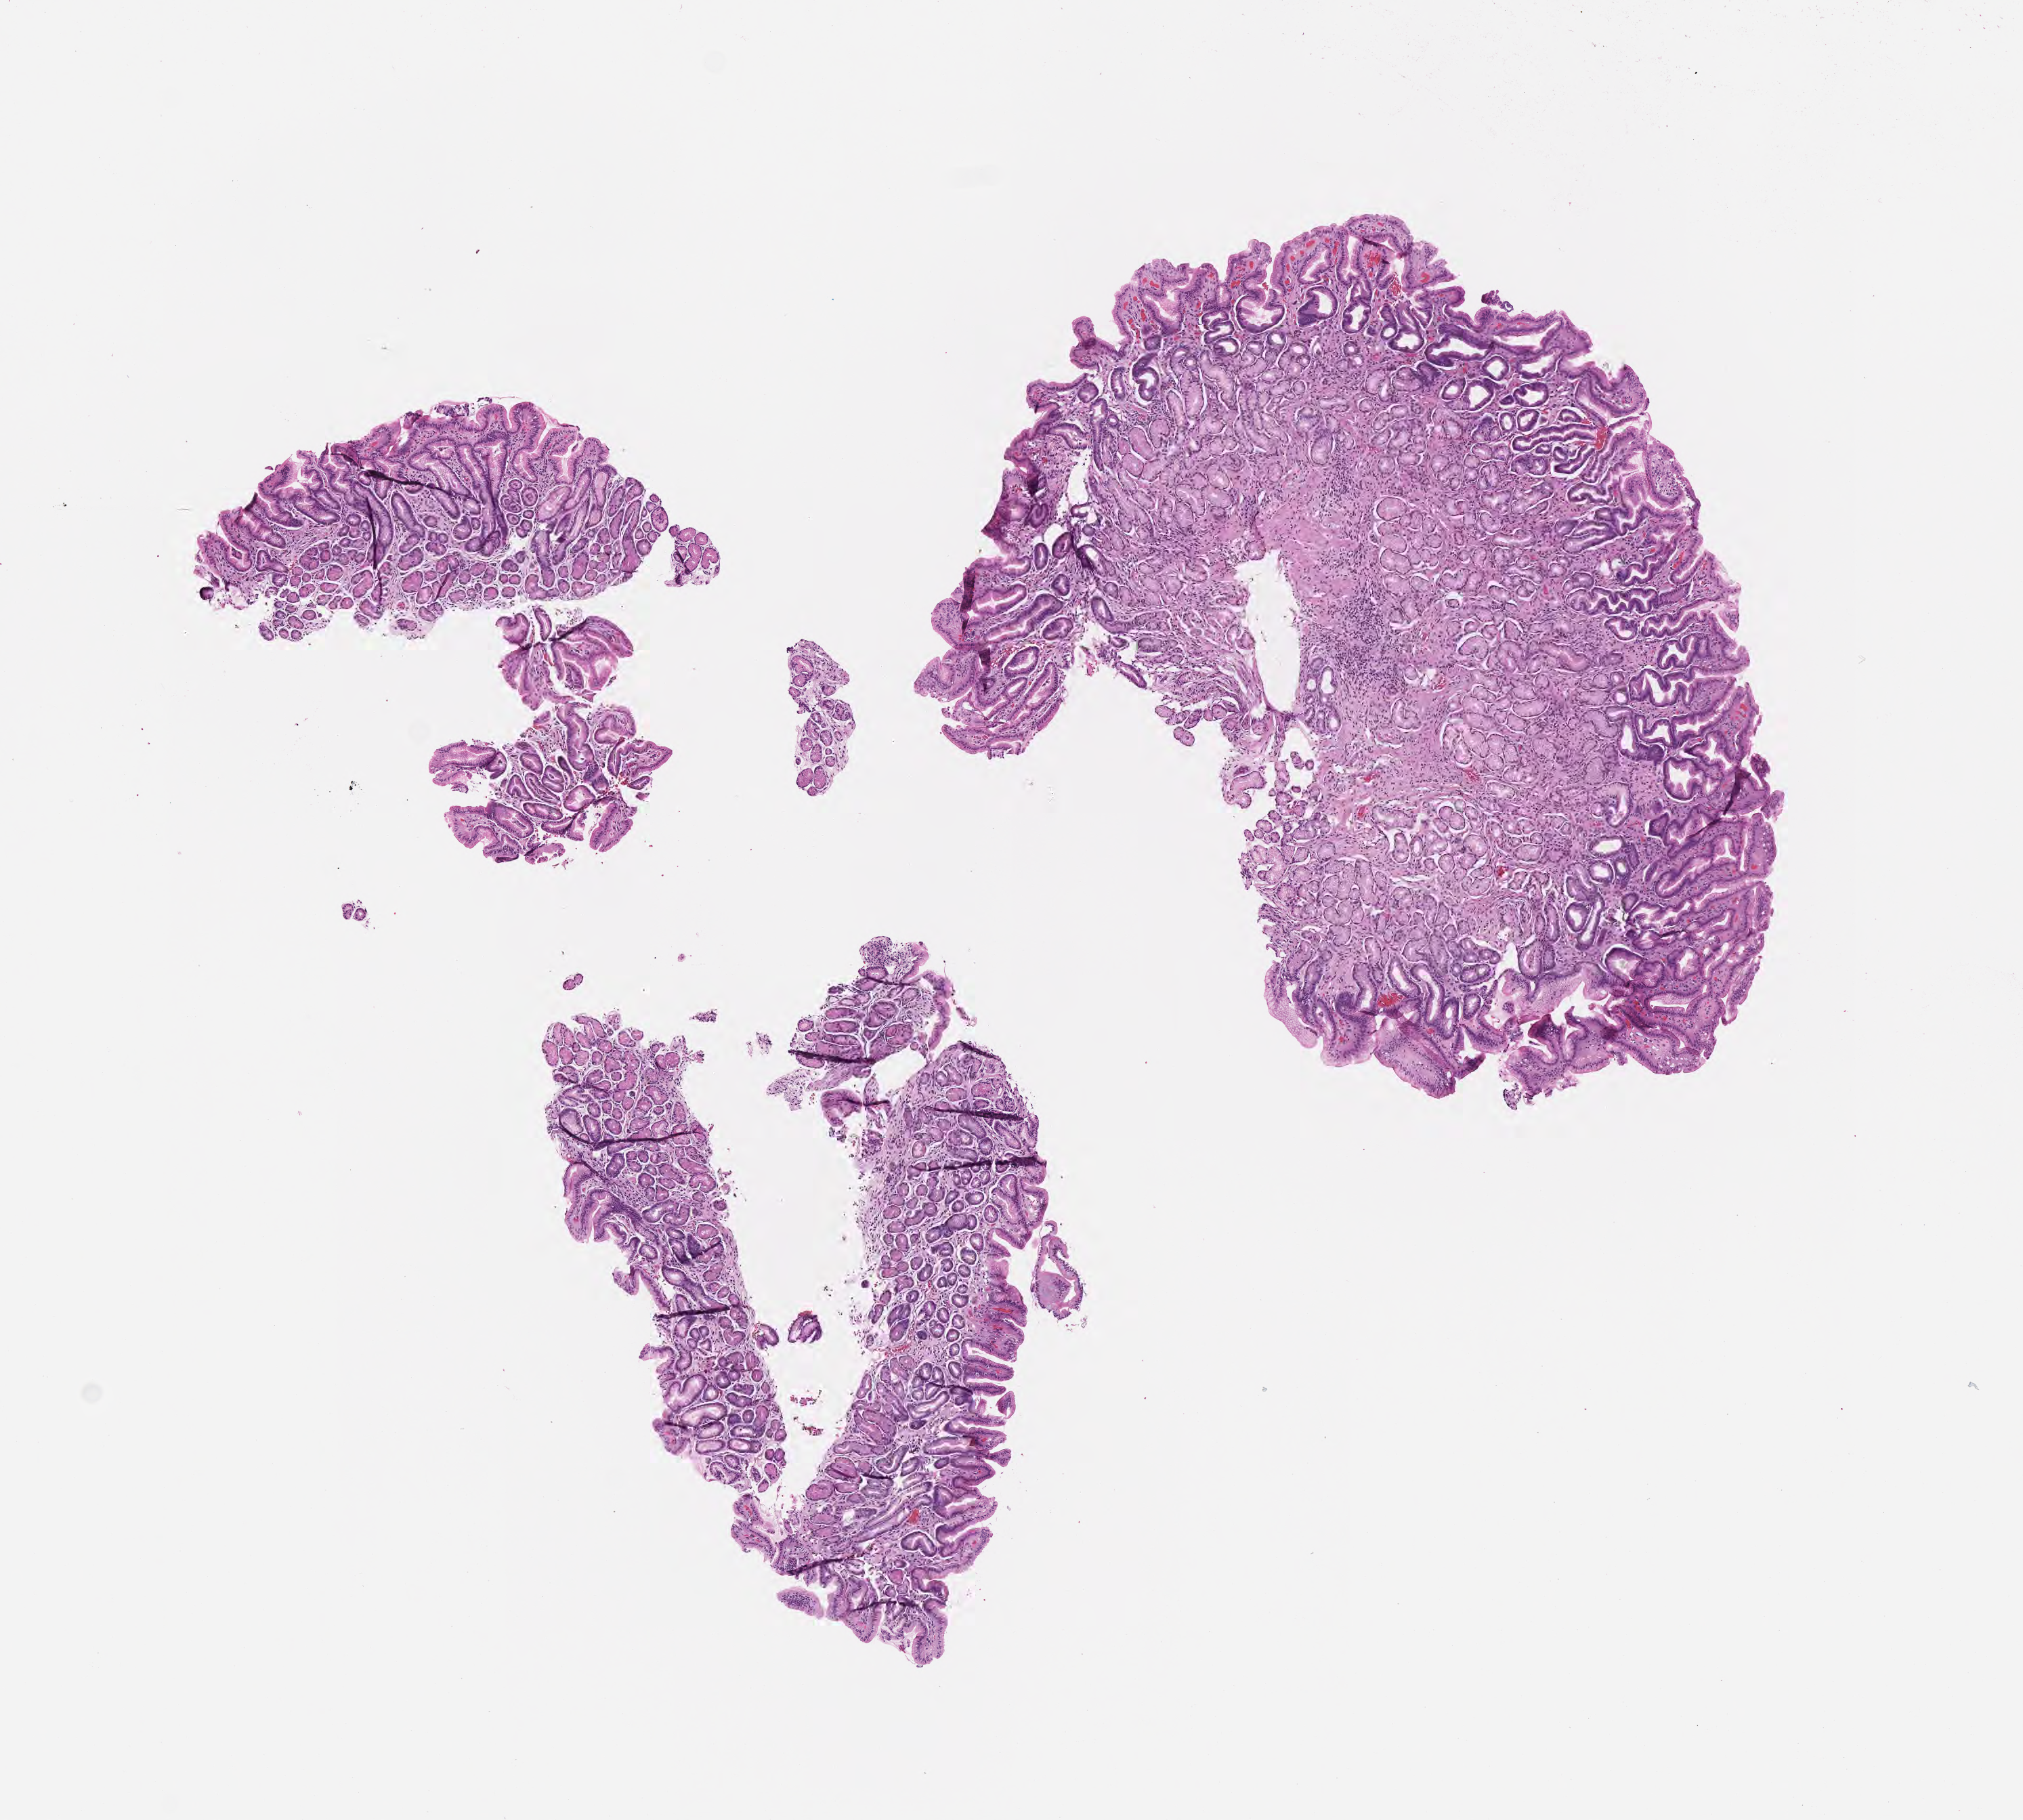
Digitized H&E-stained section, shown as a low-resolution overview of the whole scanned area (about 6.0 x 5.4 mm), formalin-fixed paraffin-embedded section, specimen: normal-tissue sample (non-tumor) from a patient with burkitt lymphoma, NOS. Patient: female, age 34 years. Composition of this section per pathologist review: tumor cells 0%, tumor nuclei 0%, stromal cells 10%, necrosis 0%, normal cells 90%. Infiltration values recorded for this section: lymphocyte infiltration 80%, monocyte infiltration 5%, neutrophil infiltration 5%.
This section: non-tumor tissue sample; the patient's diagnosis is given above. Section: top of the tissue portion.